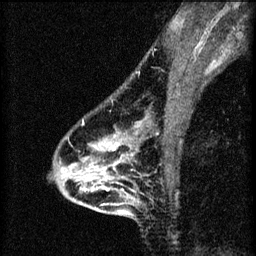
Breast MRI (dynamic contrast-enhanced), one sagittal slice; position 44 of 60 along the scan axis; 3 images stored at this slice position (order not interpretable as contrast timing); 1.5 T; TE 4.2 ms, TR 8.2 ms; 2 mm slice thickness; 256 × 256 image matrix, field of view 180 × 180 mm. Female patient, age 46 years.
Annotated regions visible in this slice (semi-automatically segmented with operator editing):
- analysis volume of interest (the breast-tissue region the enhancement analysis was run in; not a lesion): bounding box <55,116,148,209> (left, top, right, bottom; pixels)
- tumour enhancement mask (voxels above the 70 % enhancement threshold inside the analysis volume of interest): <83,122,122,191>